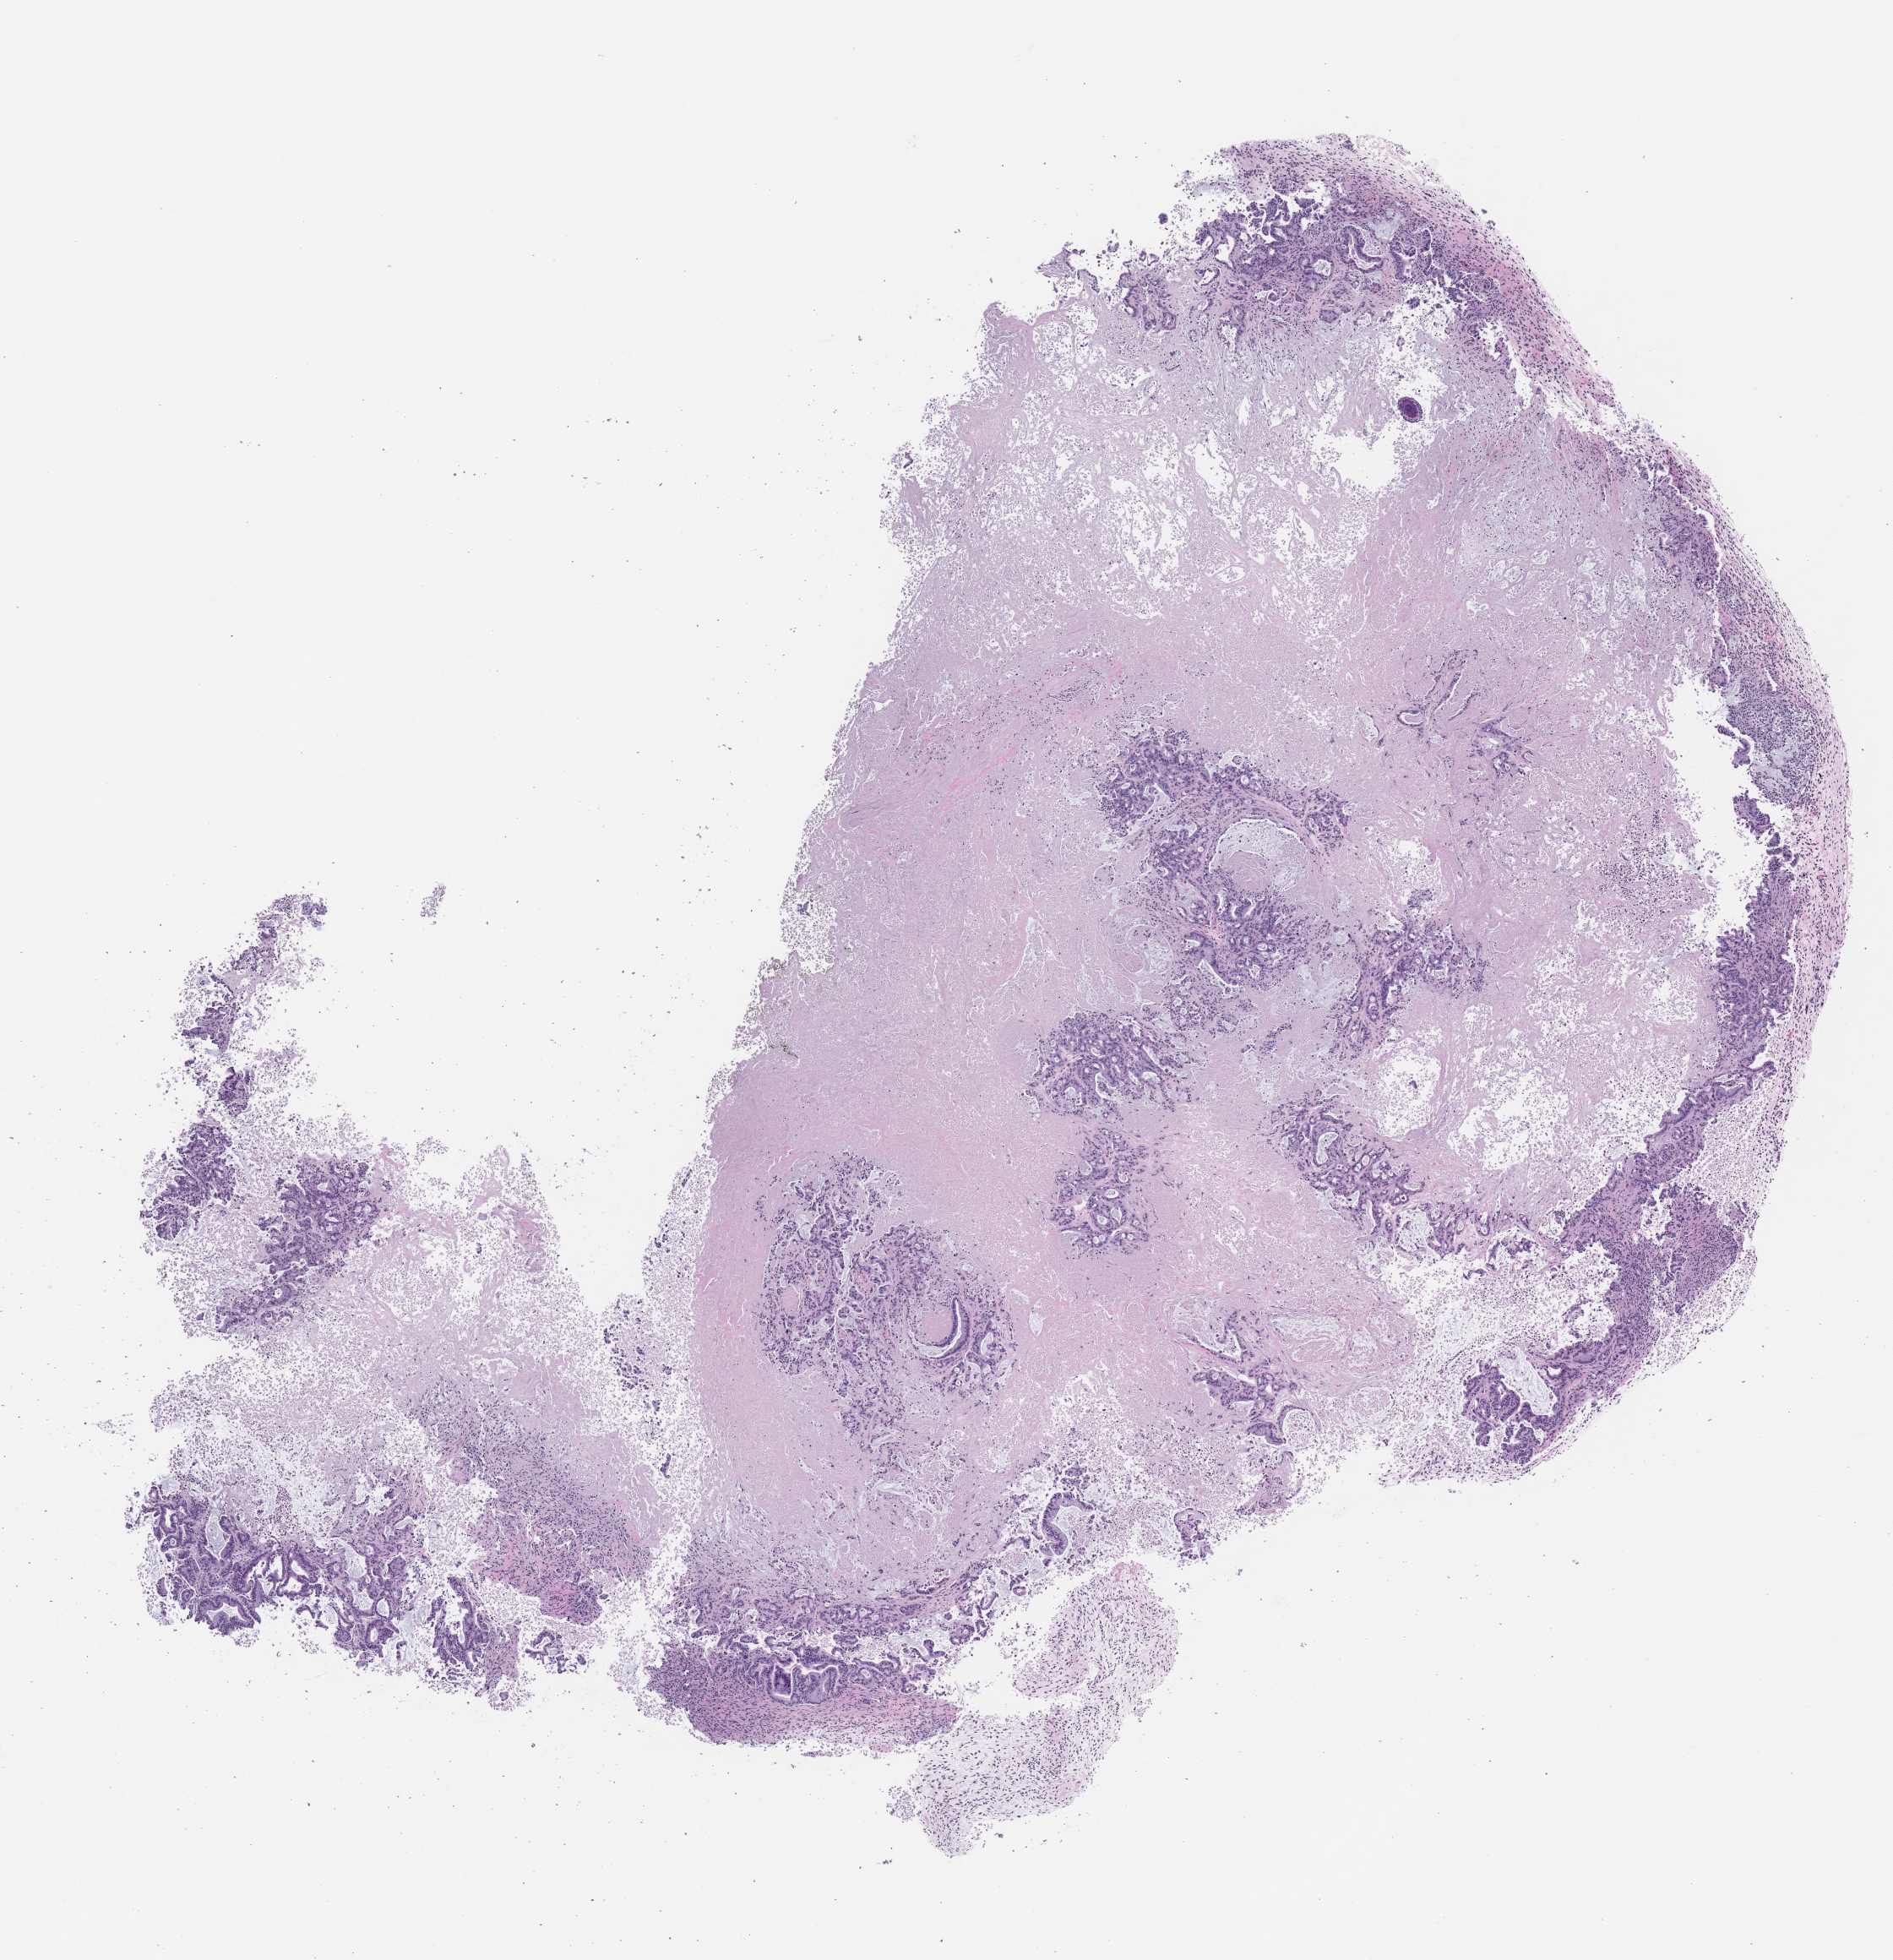
Whole-slide image, hematoxylin and eosin (H&E): patient-derived xenograft (human tumor grown in a mouse), passage 3, low-resolution overview of the scanned area, about 9.0 x 9.3 mm. FFPE section. Originating tumor site category: pancreas.
Originating patient diagnosis: Pancreatic Adenocarcinoma.